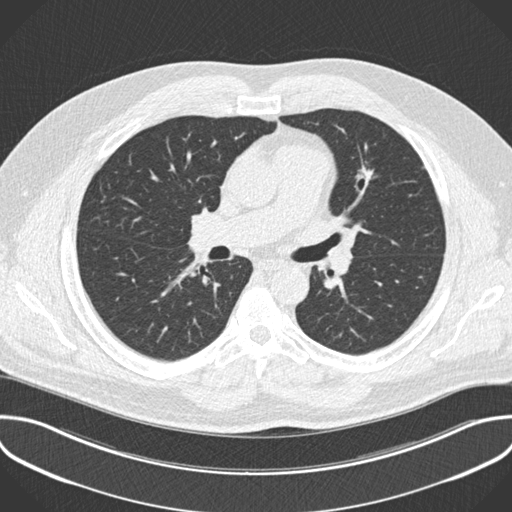
Low-dose screening chest CT, one axial slice. Position 125 of 201 along the scan axis. Reconstruction kernel B30f. 120 kVp. Lung window (W 1500 / L -600 HU). 2 mm slice thickness. 512 × 512 image matrix.
Annotated regions visible in this slice (manually delineated by an expert):
- lesion 1 (tumor, upper lobe of left lung): bounding box (x1, y1, x2, y2) in pixels: (357, 169, 373, 184)